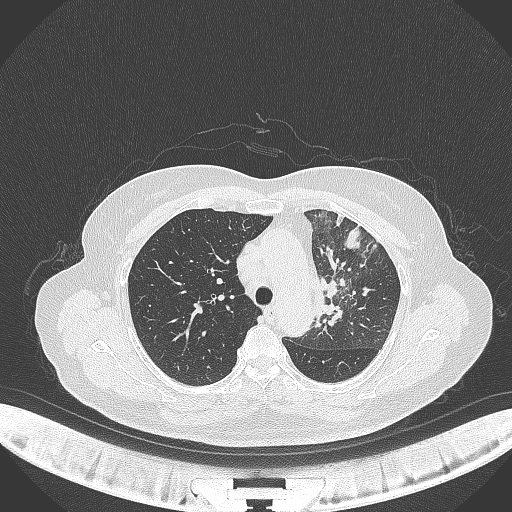
Chest CT, one axial slice. Slice 246 of 382 in the series (ordered by position). Lung window (W 1500 / L -600 HU). 1 mm slice thickness. 512 × 512 image matrix, field of view 400 × 400 mm. Female patient, age 64 years. Case-level facts recorded for this patient, not image findings: clinical TNM (as recorded): T2a N2 M0.
Annotated regions visible in this slice (rectangle marked by the reading radiologist):
- lung tumour (recorded histology: adenocarcinoma): bounding box [x1, y1, x2, y2] px = [312, 271, 345, 332]
- lung tumour (recorded histology: adenocarcinoma): [340, 222, 369, 256]